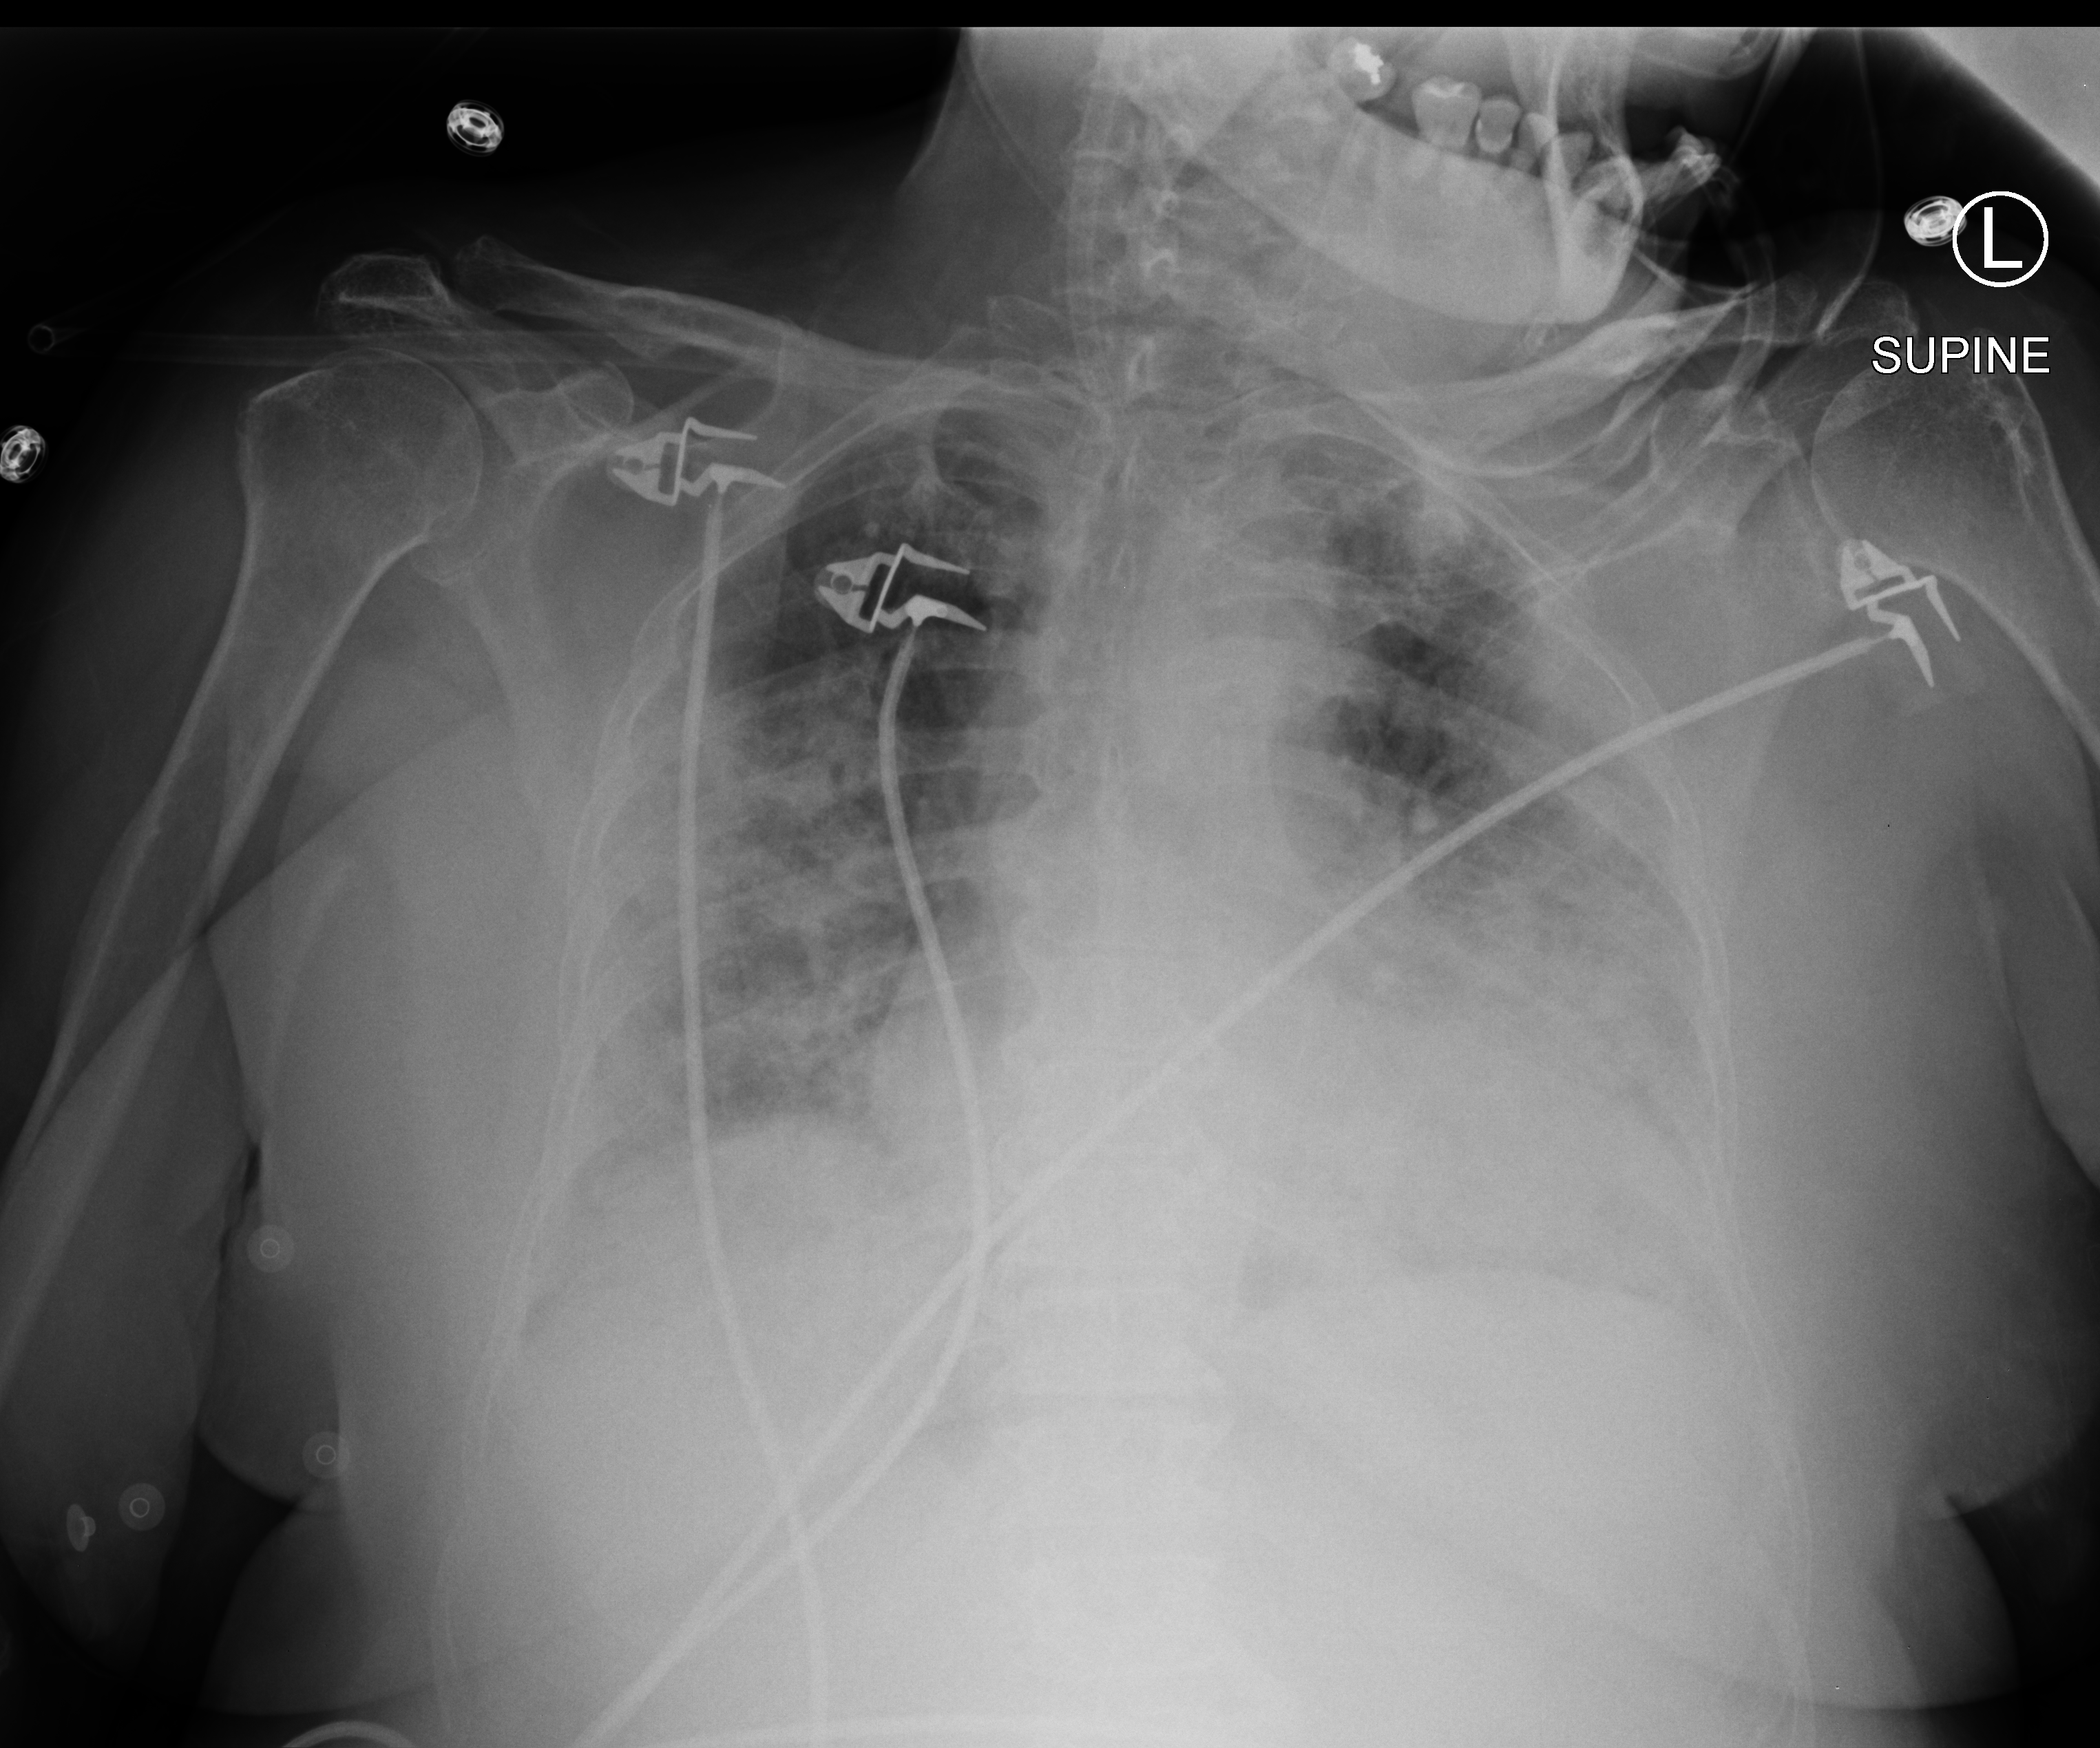
Bedside chest radiograph (computed radiography); anteroposterior (AP) projection. Female patient hospitalised with COVID-19, age 75–90 years.
Hospital-stay facts (about this admission, not read from this image; timing relative to this image not recorded):
- COPD (admission record): yes